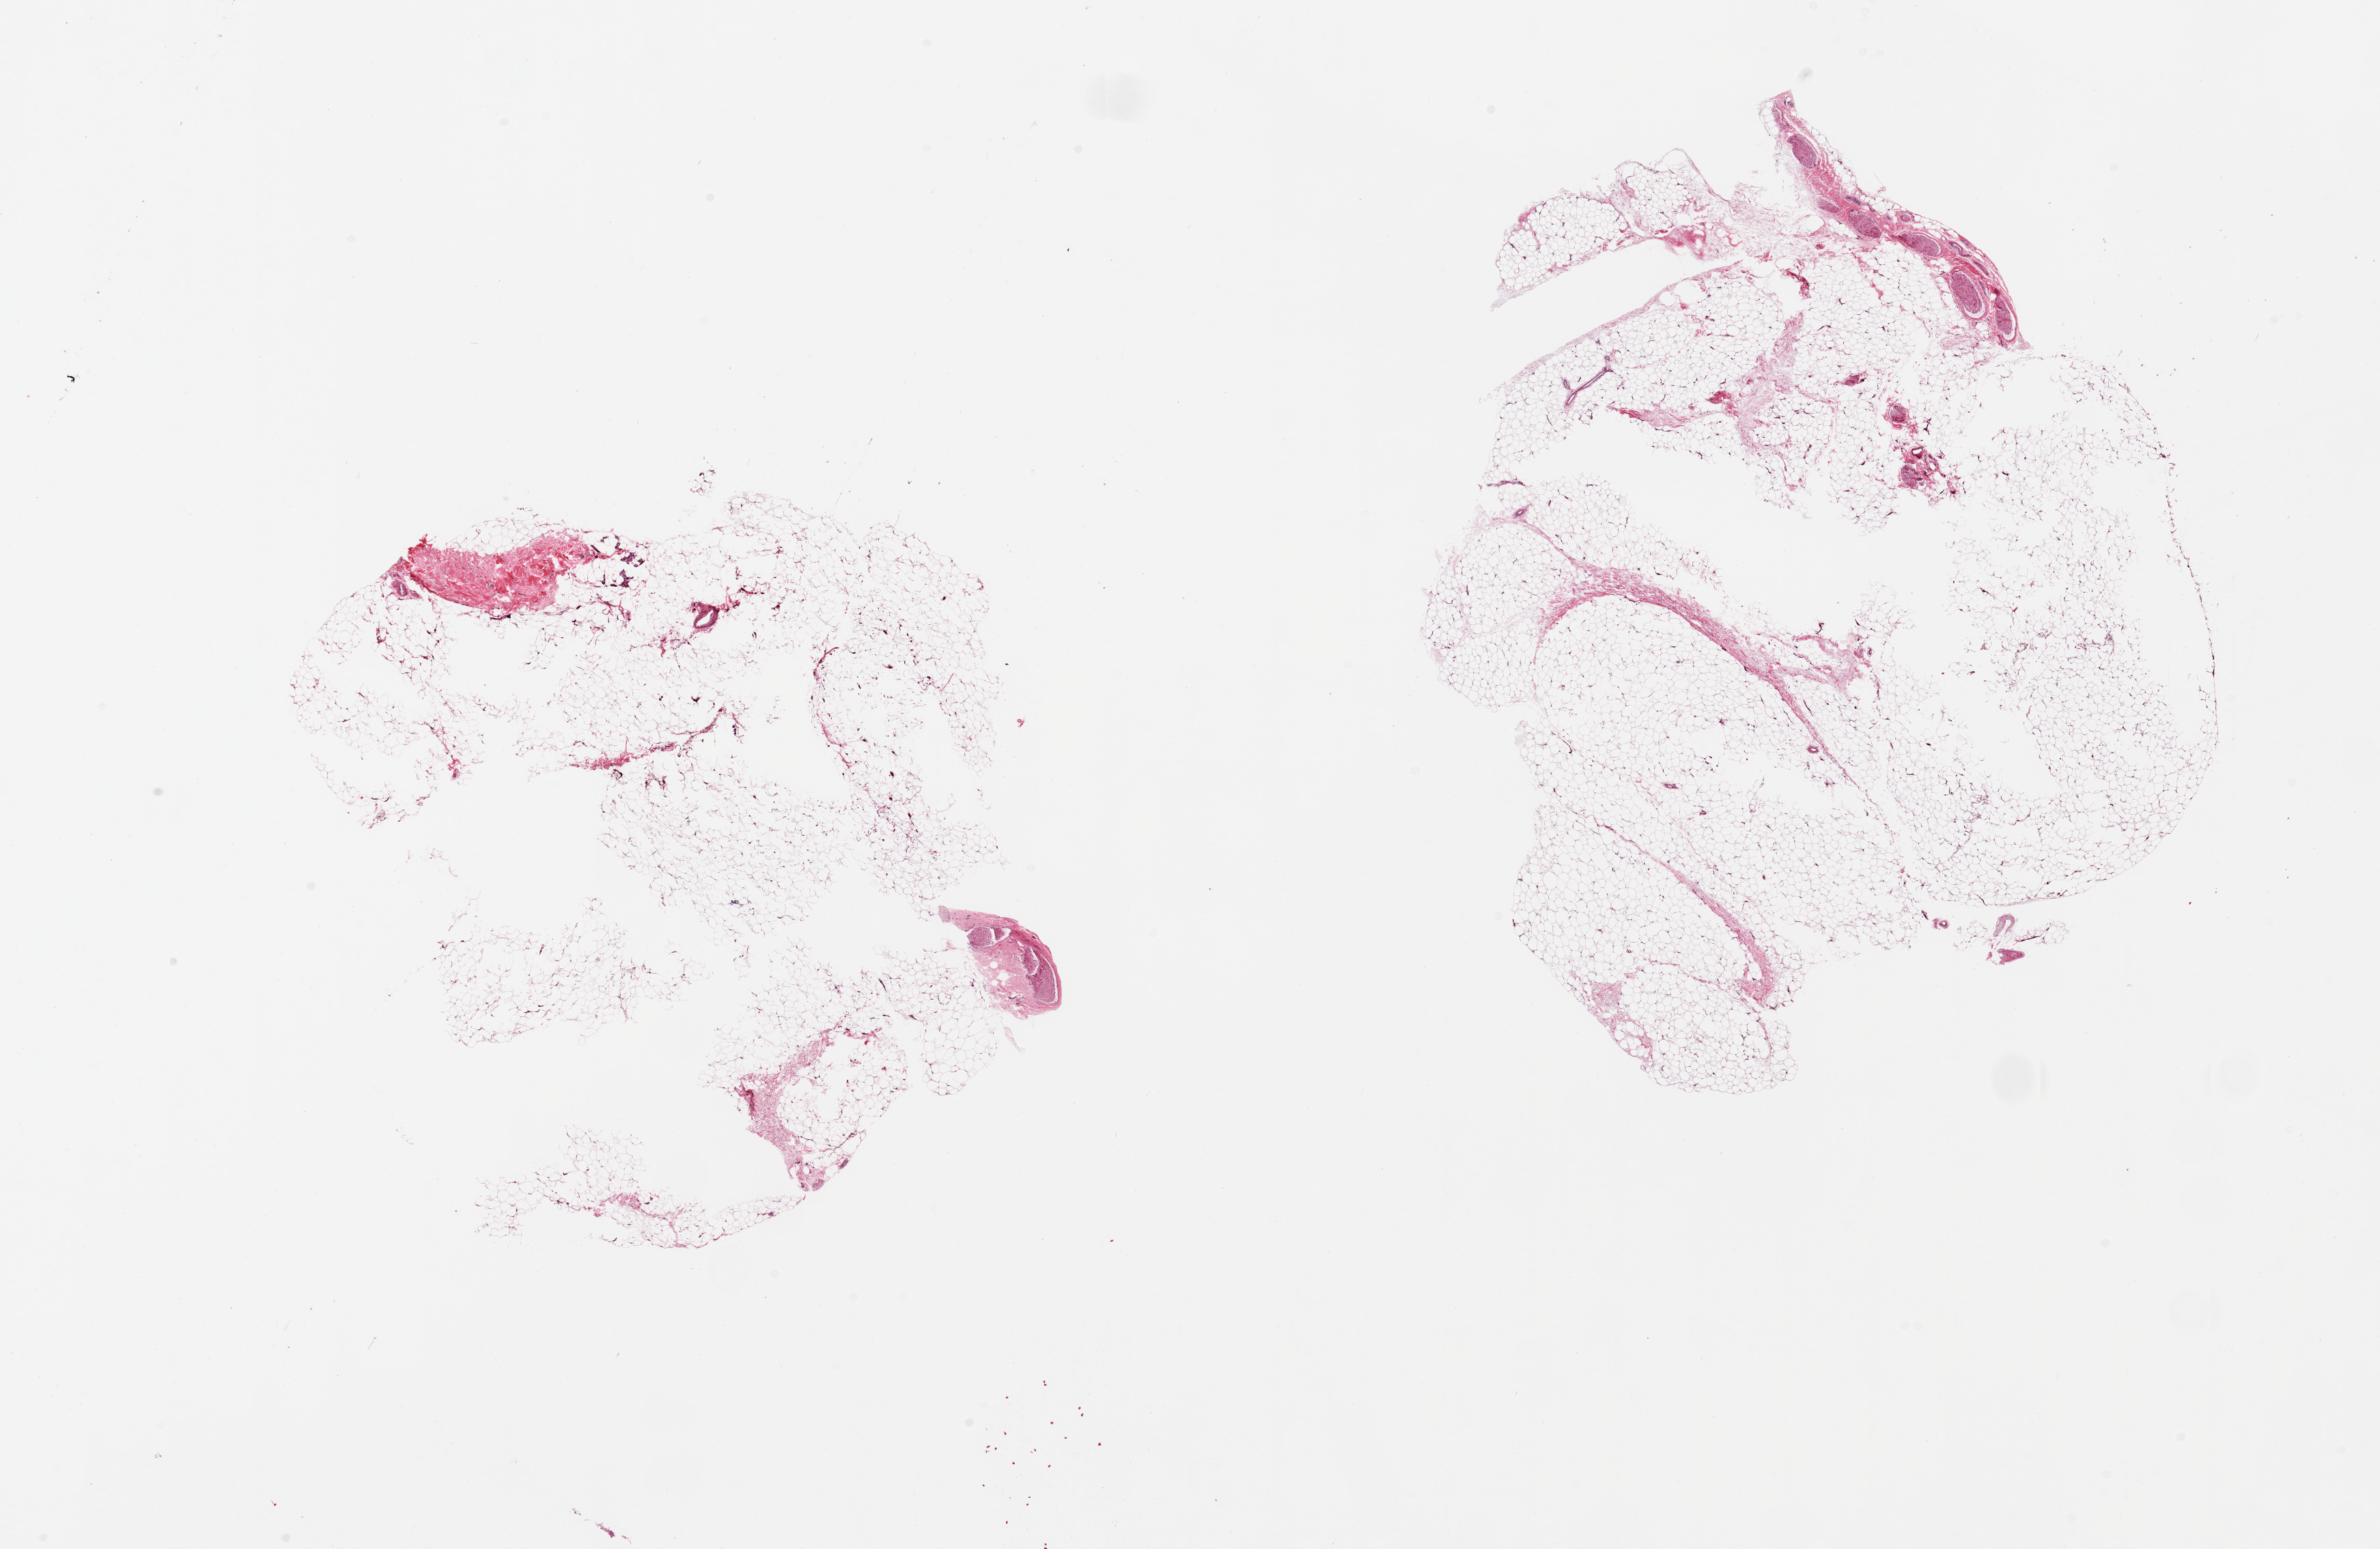
Digitized hematoxylin and eosin (H&E)-stained section — a low-resolution overview of the entire scanned area, about 27.6 x 17.9 mm (from a 20x scan); PAXgene-fixed paraffin-embedded (PFPE) section; section of adipose tissue (target tissue); donor tissue sample. Donor: female.
Review note (as recorded): 2 pieces: both contain small foci of nerves at edge; central holes.